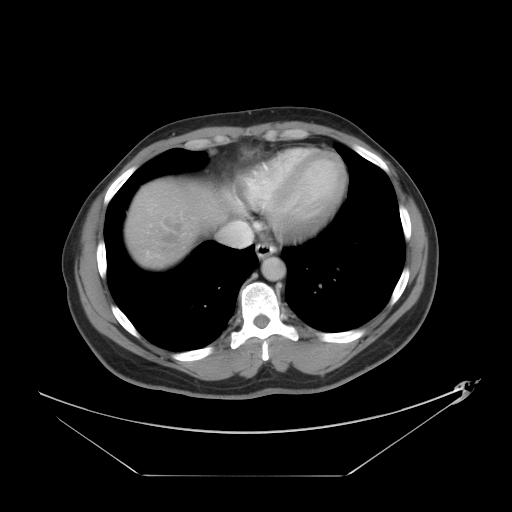
Contrast-enhanced abdominal CT, one axial slice. Position 39 of 44 along the scan axis. Intravenous contrast given. Soft-tissue window (W 400 / L 40 HU). 512 × 512 image matrix, field of view 466 × 466 mm. Male patient, age 49 years. From the clinical record (not read from this slice): diagnosis: colorectal cancer liver metastases, imaged before liver resection; multiple liver metastases: no; largest metastasis: 8.5 cm; disease in both lobes: yes.
Structures marked on this image (expert manual segmentation):
- liver: bounding box [x1, y1, x2, y2] px = [124, 177, 236, 272]
- planned liver remnant (the part of the liver to remain after resection): [210, 182, 237, 224]
- liver metastasis: [162, 219, 183, 244]